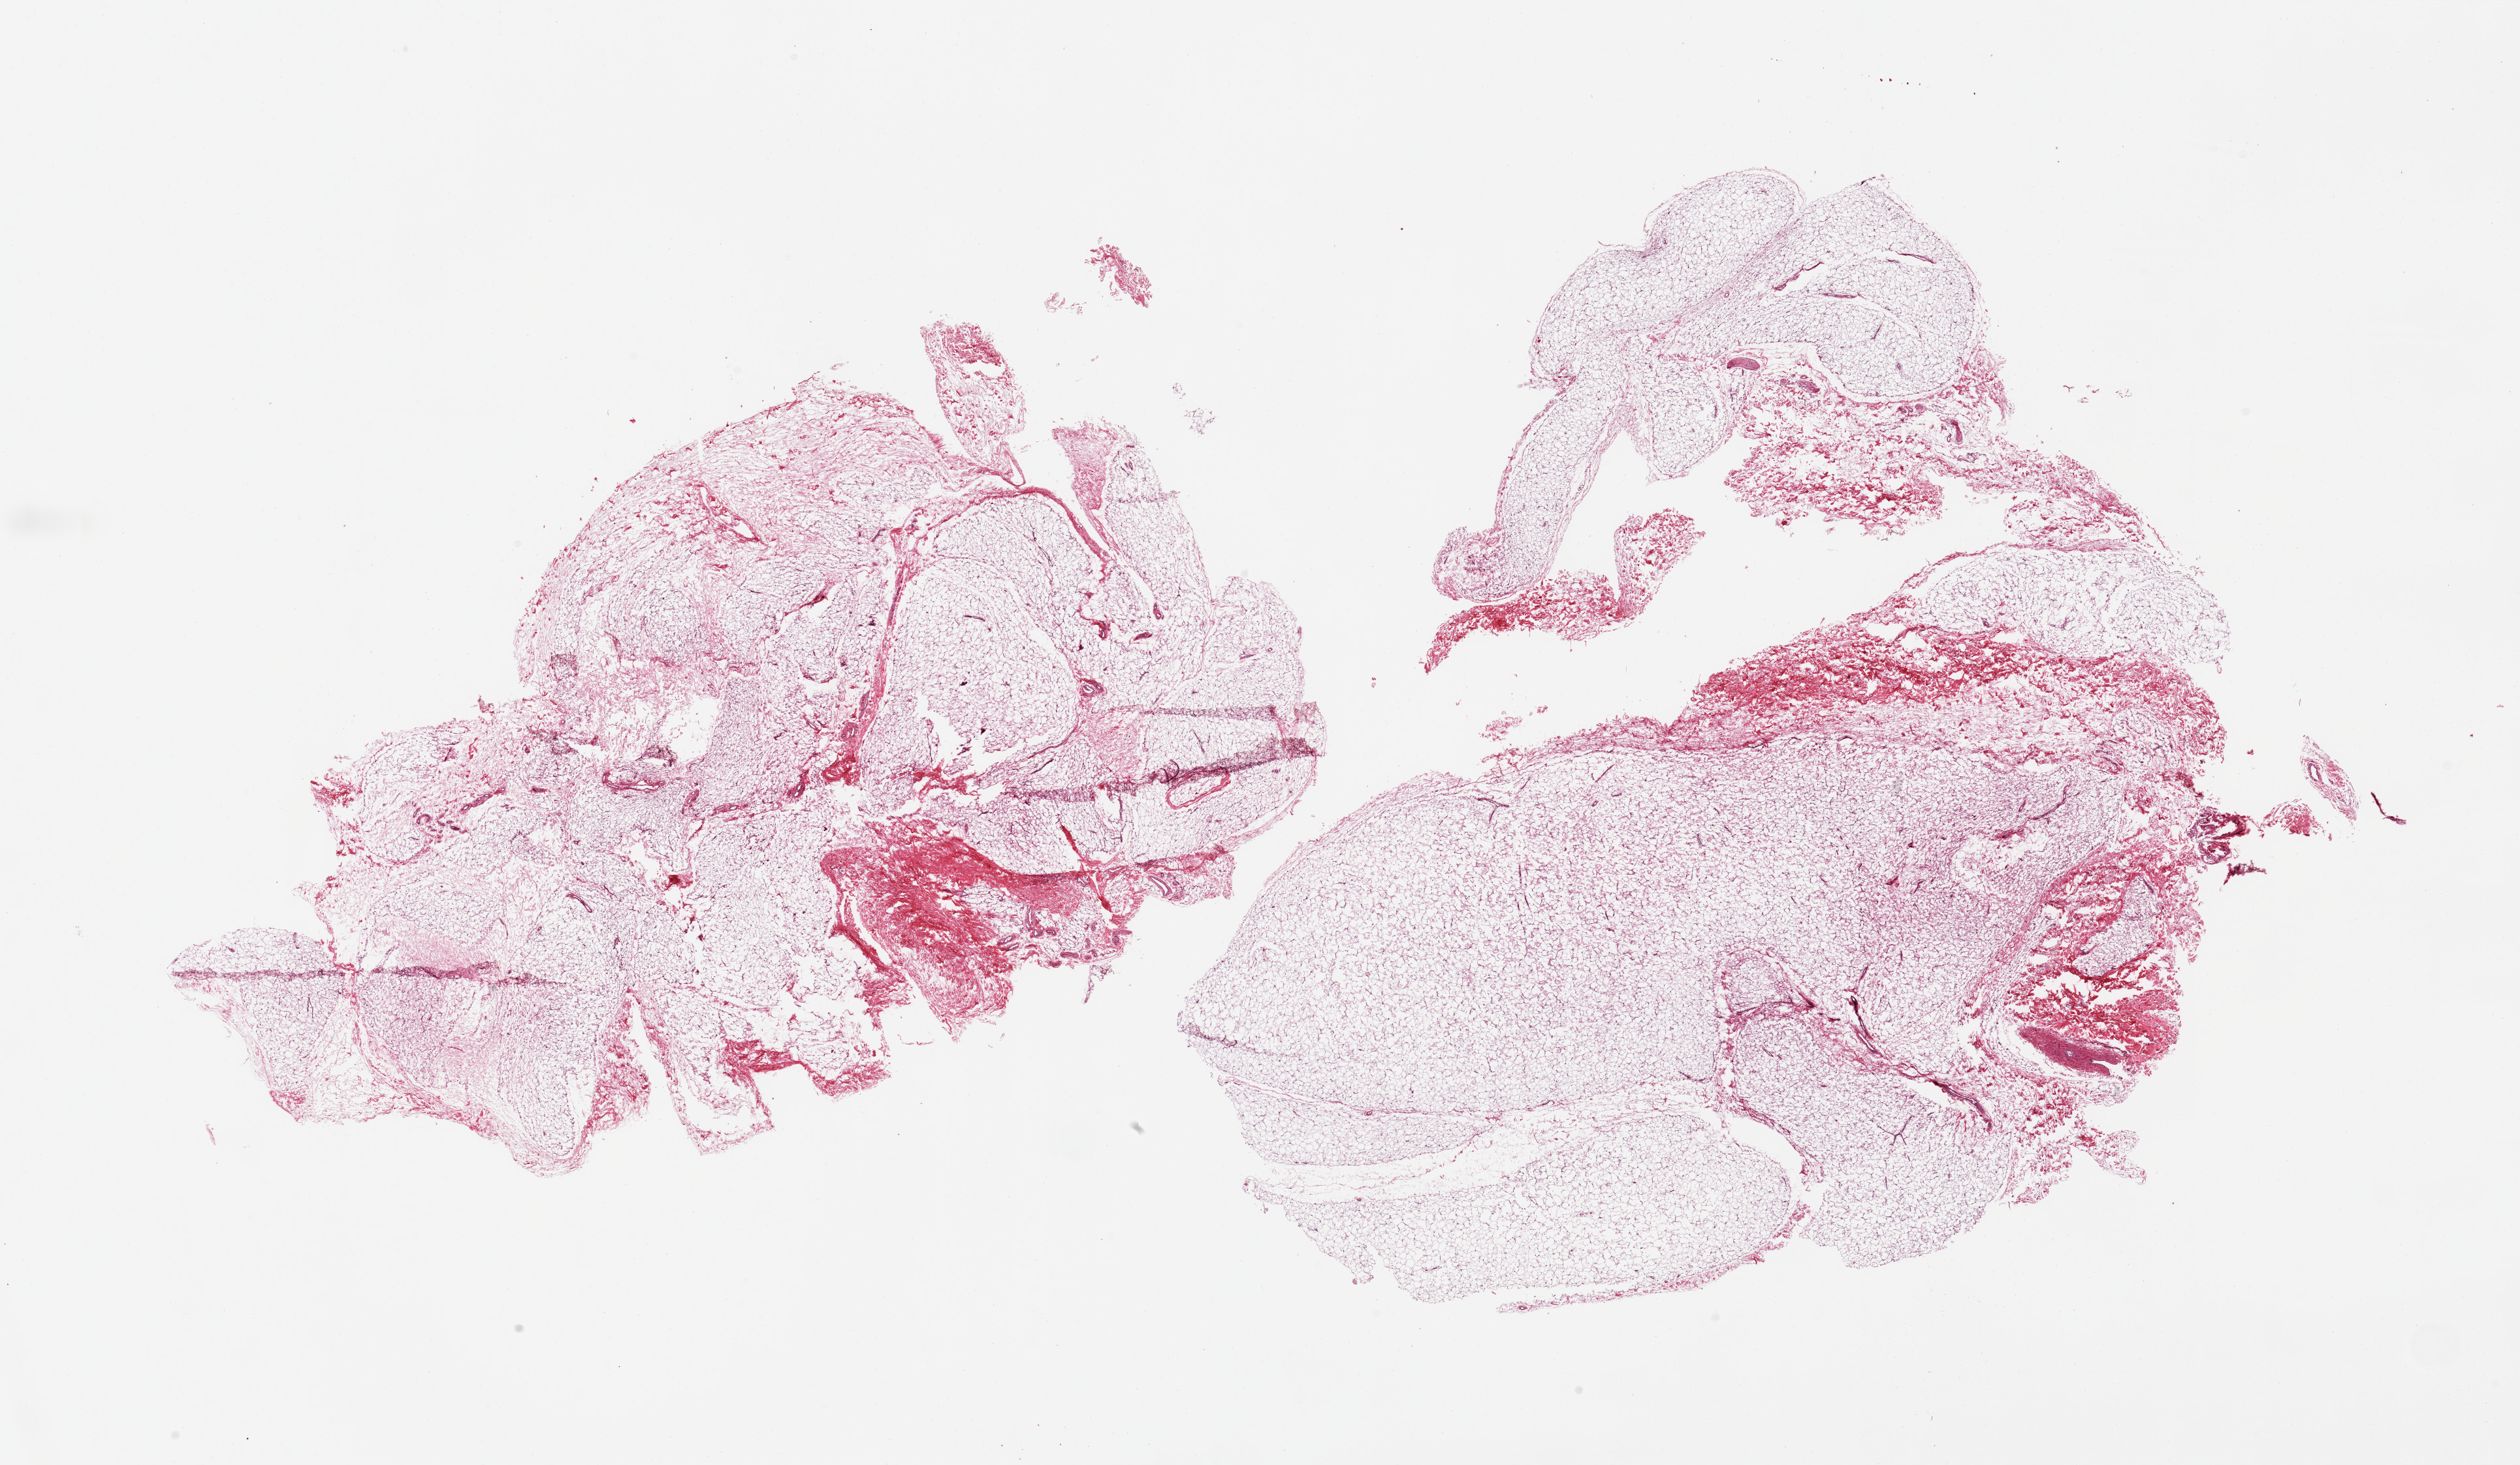
H&E whole-slide image, whole scanned area (about 30.5 x 17.7 mm) shown as a low-resolution overview; PAXgene-fixed, paraffin-embedded tissue; section of breast (target tissue); donor tissue sample.
Reviewer comment on this tissue sample: 2 pieces; over-sized, predominantly fat with ~15% fibrous stroma, no ducts/lobules in this section.